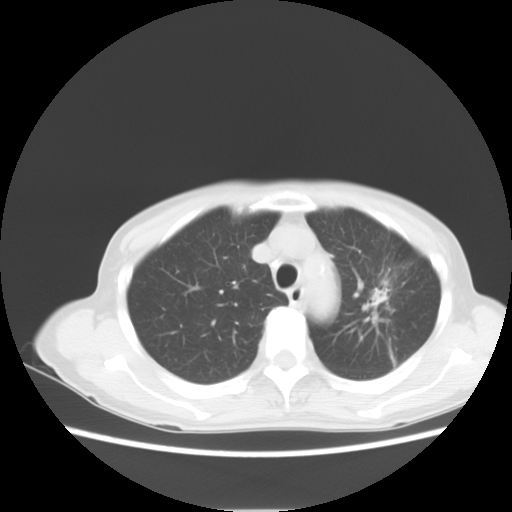
Chest CT, one axial slice. Position 7 of 14 along the scan axis. Reconstruction kernel STANDARD. 120 kVp. Lung window (W 1500 / L -600 HU). 5 mm slice thickness. 512 × 512 image matrix, field of view 350 × 350 mm. Patient: female, 71 years. From the clinical record (not read from this slice): clinical TNM (as recorded): T2 N0 M0.
Annotated regions visible in this slice (rectangle marked by the reading radiologist):
- lung tumour (recorded histology: adenocarcinoma): bounding box [x1, y1, x2, y2] px = [367, 281, 390, 313]